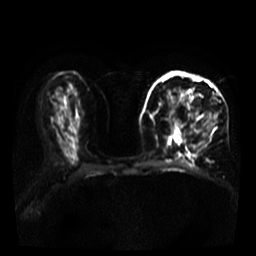
Breast MRI, one axial slice; position 17 of 39 along the scan axis; diffusion-weighted series; image 2 of 4 stored at this slice position (different b-values; order by instance number); 3 T; 5 mm slice thickness; 256 × 256 image matrix. Female patient.
Annotated regions visible in this slice (expert manual segmentation):
- tumour on diffusion-weighted imaging: bounding box <176,90,190,127> (left, top, right, bottom; pixels)